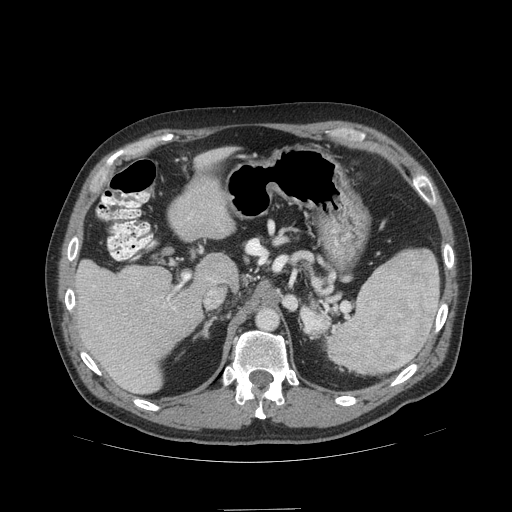
Contrast-enhanced abdominal CT (liver protocol), one axial slice. Position 66 of 99 along the scan axis. 140 kVp. Soft-tissue window (W 400 / L 40 HU). 2.5 mm slice thickness. 512 × 512 image matrix. From the clinical record (not read from this slice): diagnosis: hepatocellular carcinoma (patient treated with transarterial chemoembolisation; whether this scan precedes or follows treatment is not stated here); TNM stage (as recorded): Stage-I; Child-Pugh class: A; tumour differentiation: no biopsy; tumour nodularity: uninodular.
Structures marked on this image (semi-automatically segmented with operator editing):
- liver parenchyma outside the tumour (the mass and vessels are separate outlines, so this box may not span the whole liver): box from (x=72, y=260) to (x=211, y=394) px
- liver vessels: (x=92, y=285)–(x=179, y=368)